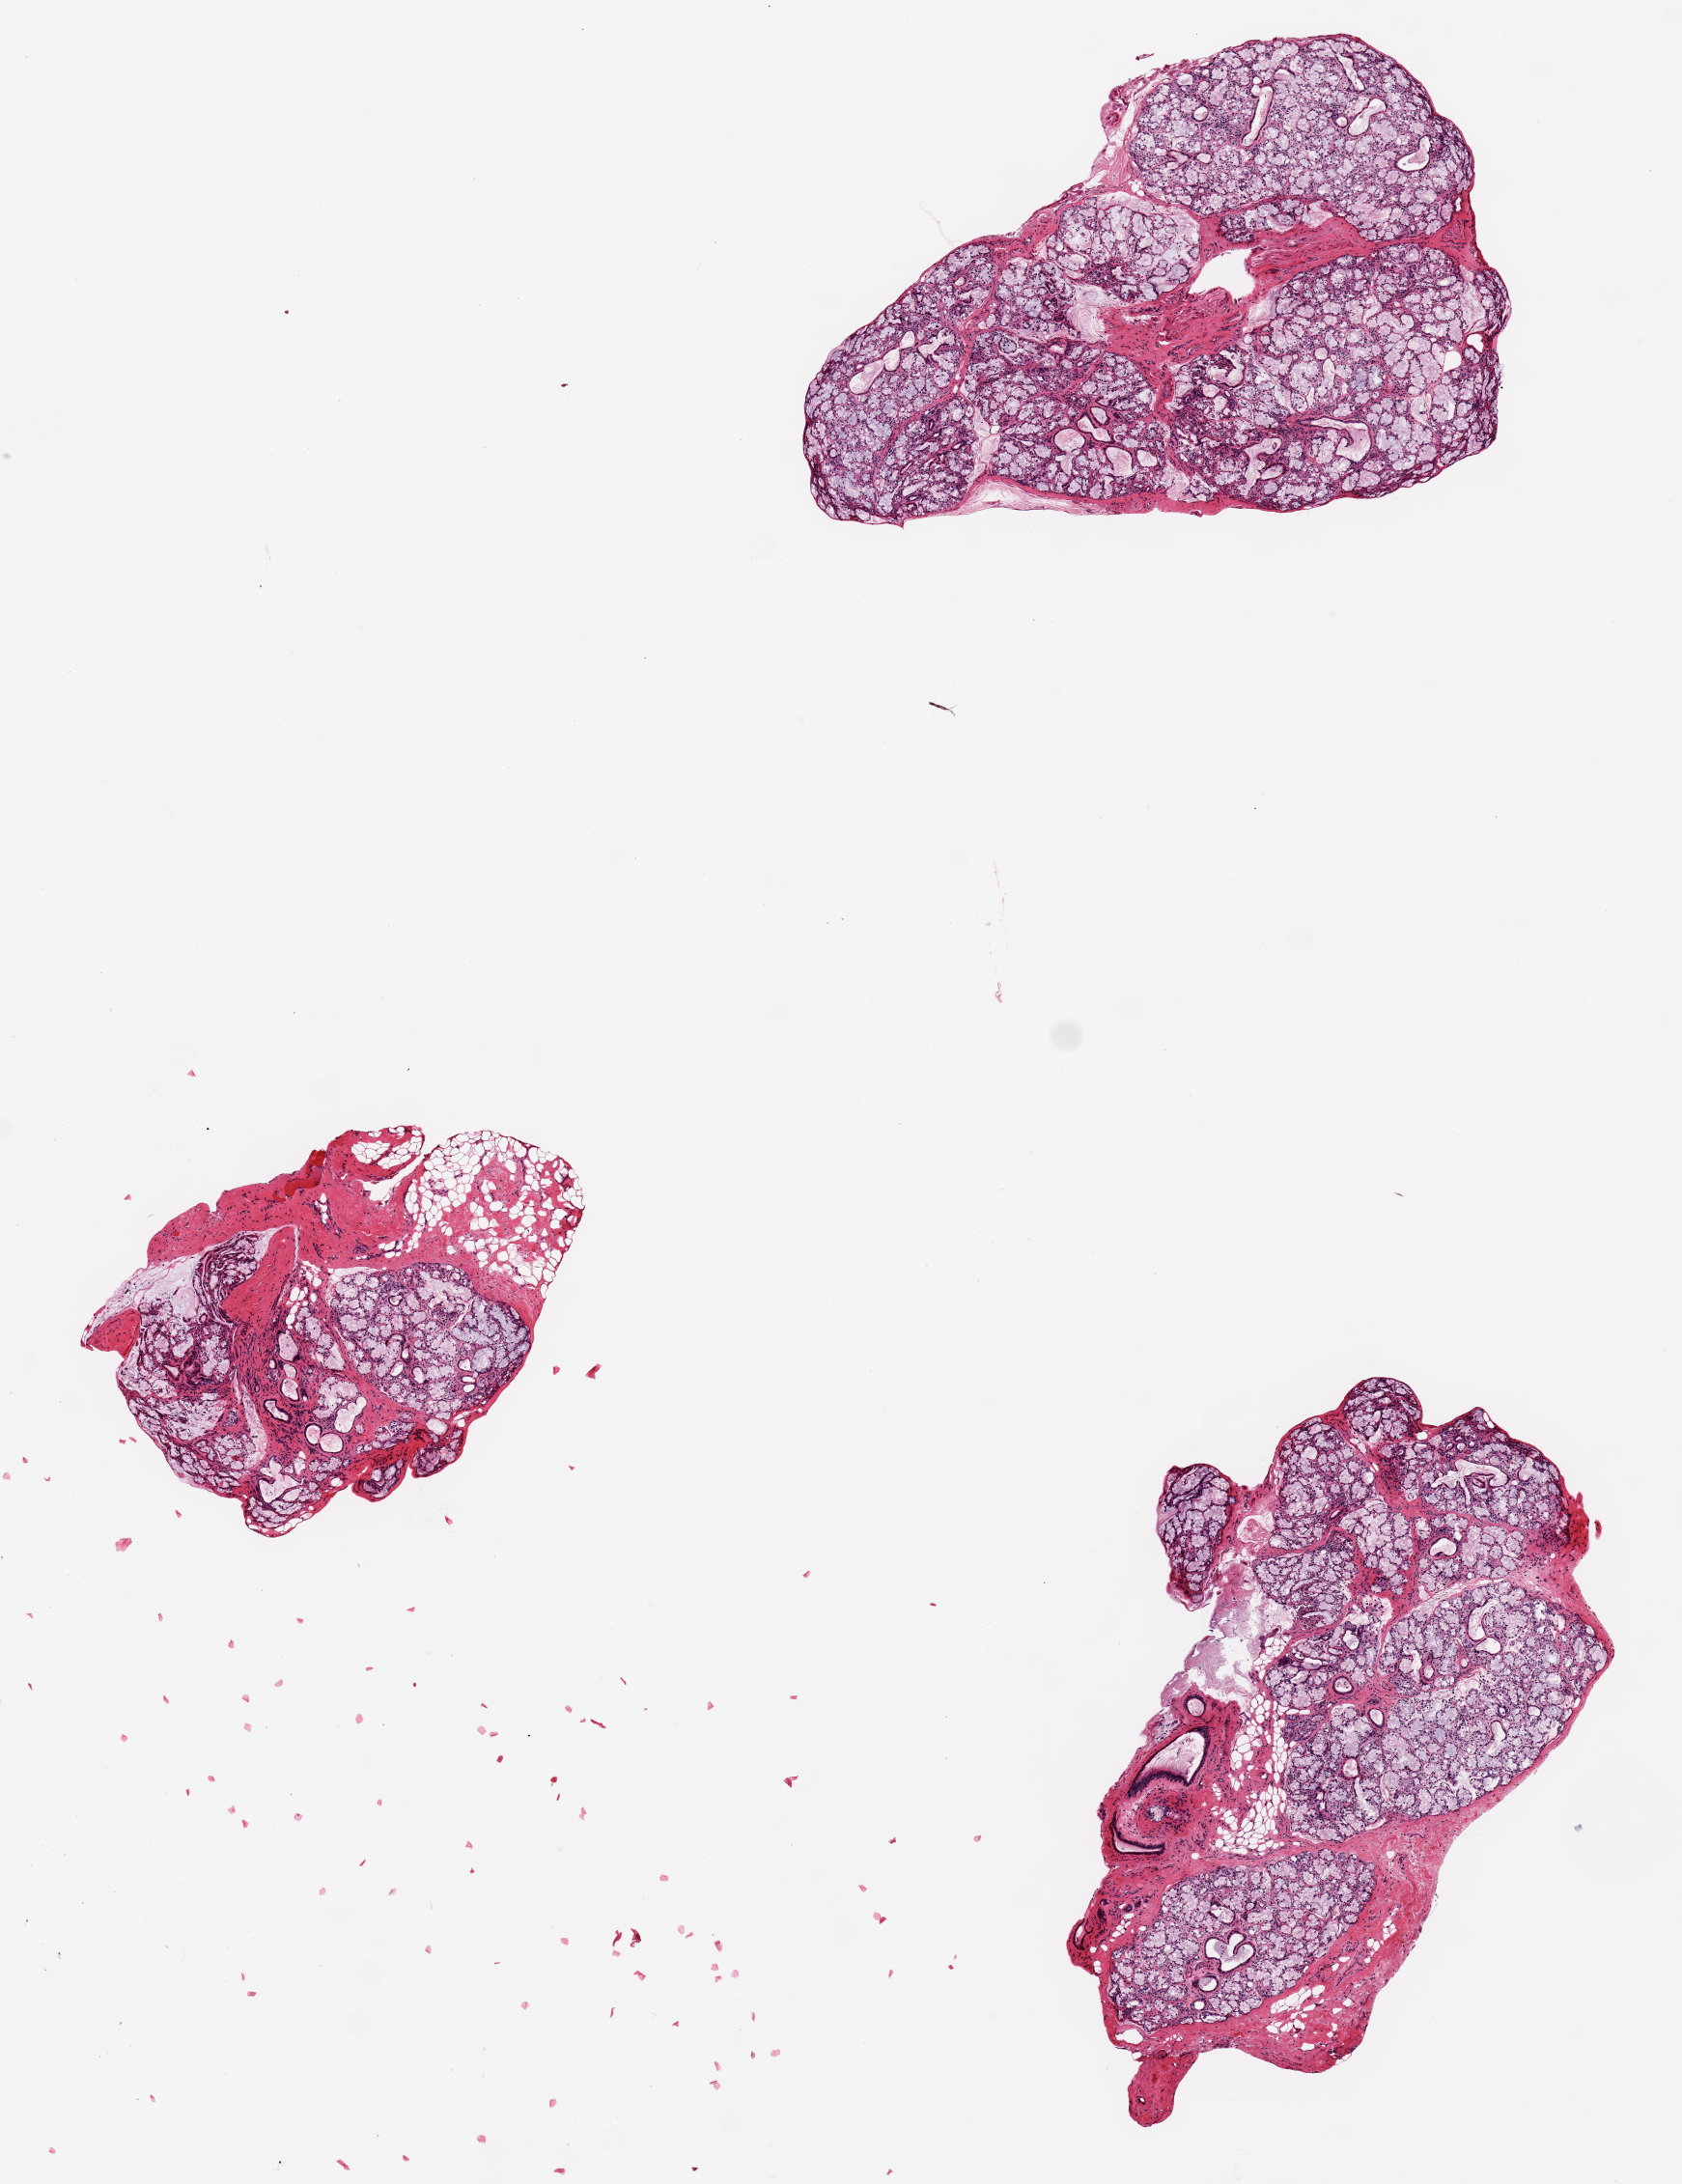
Whole-slide image, haematoxylin and eosin stain, low-resolution overview of the scanned area, about 6.9 x 8.9 mm (slide scanned at 20x); PAXgene-fixed paraffin-embedded (PFPE) section; sampled site (target tissue): minor salivary gland; donor tissue sample. Male donor.
- reviewer comment on this tissue sample: 3 pieces, up to 3x2mm; 3 good well trimmed glands; smallest has 30% (0.5 sq mm) peripheral adipose